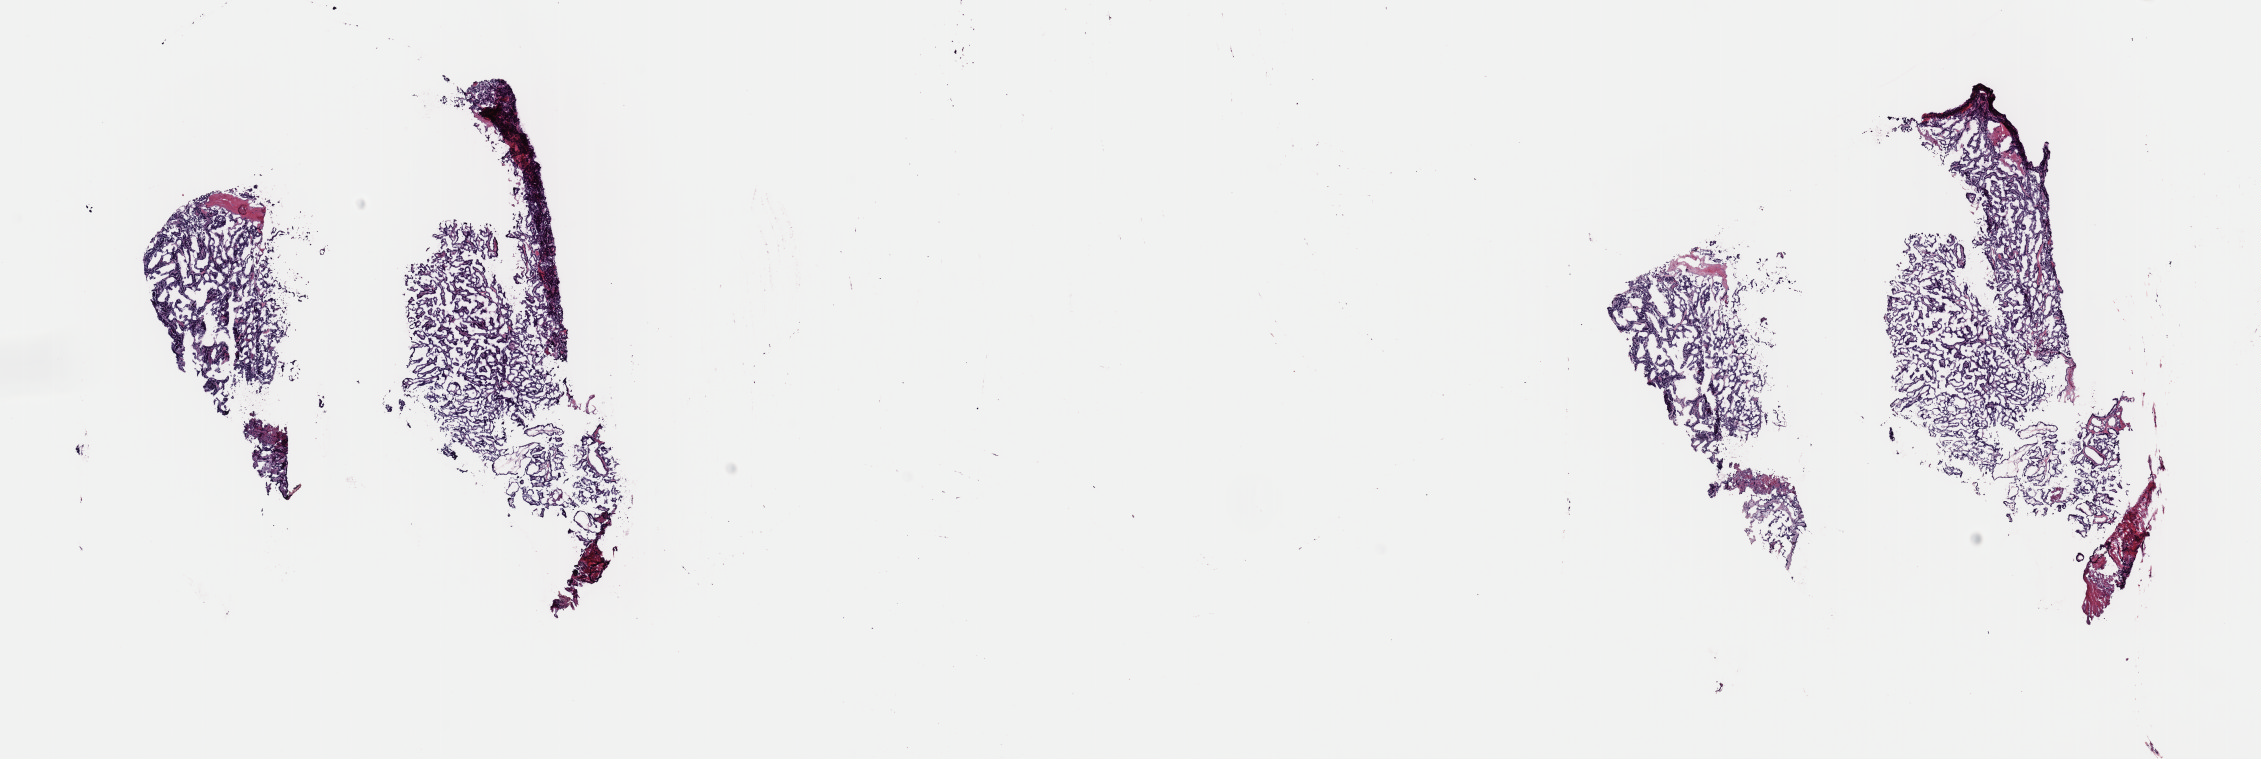
Digitized Hematoxylin and eosin (H&E) stained tissue section (whole slide), low-resolution overview of the scanned area, about 17.9 x 6.0 mm (from a 40x scan); frozen section from the top of the tissue portion; thyroid, primary tumour sample. Female, age 37 years at initial diagnosis. Composition of this section per pathologist review: tumour cells 90%, tumour nuclei 100%, normal cells 0%, stromal cells 10%, necrosis 0%. Inflammatory infiltration, as recorded: lymphocyte infiltration 0%, monocyte infiltration 0%, neutrophil infiltration 0%.
Lymph nodes positive (case pathology): 4 of 7 examined. Diagnosis: Papillary adenocarcinoma, NOS (thyroid gland). AJCC pathologic stage: I (5th edition).